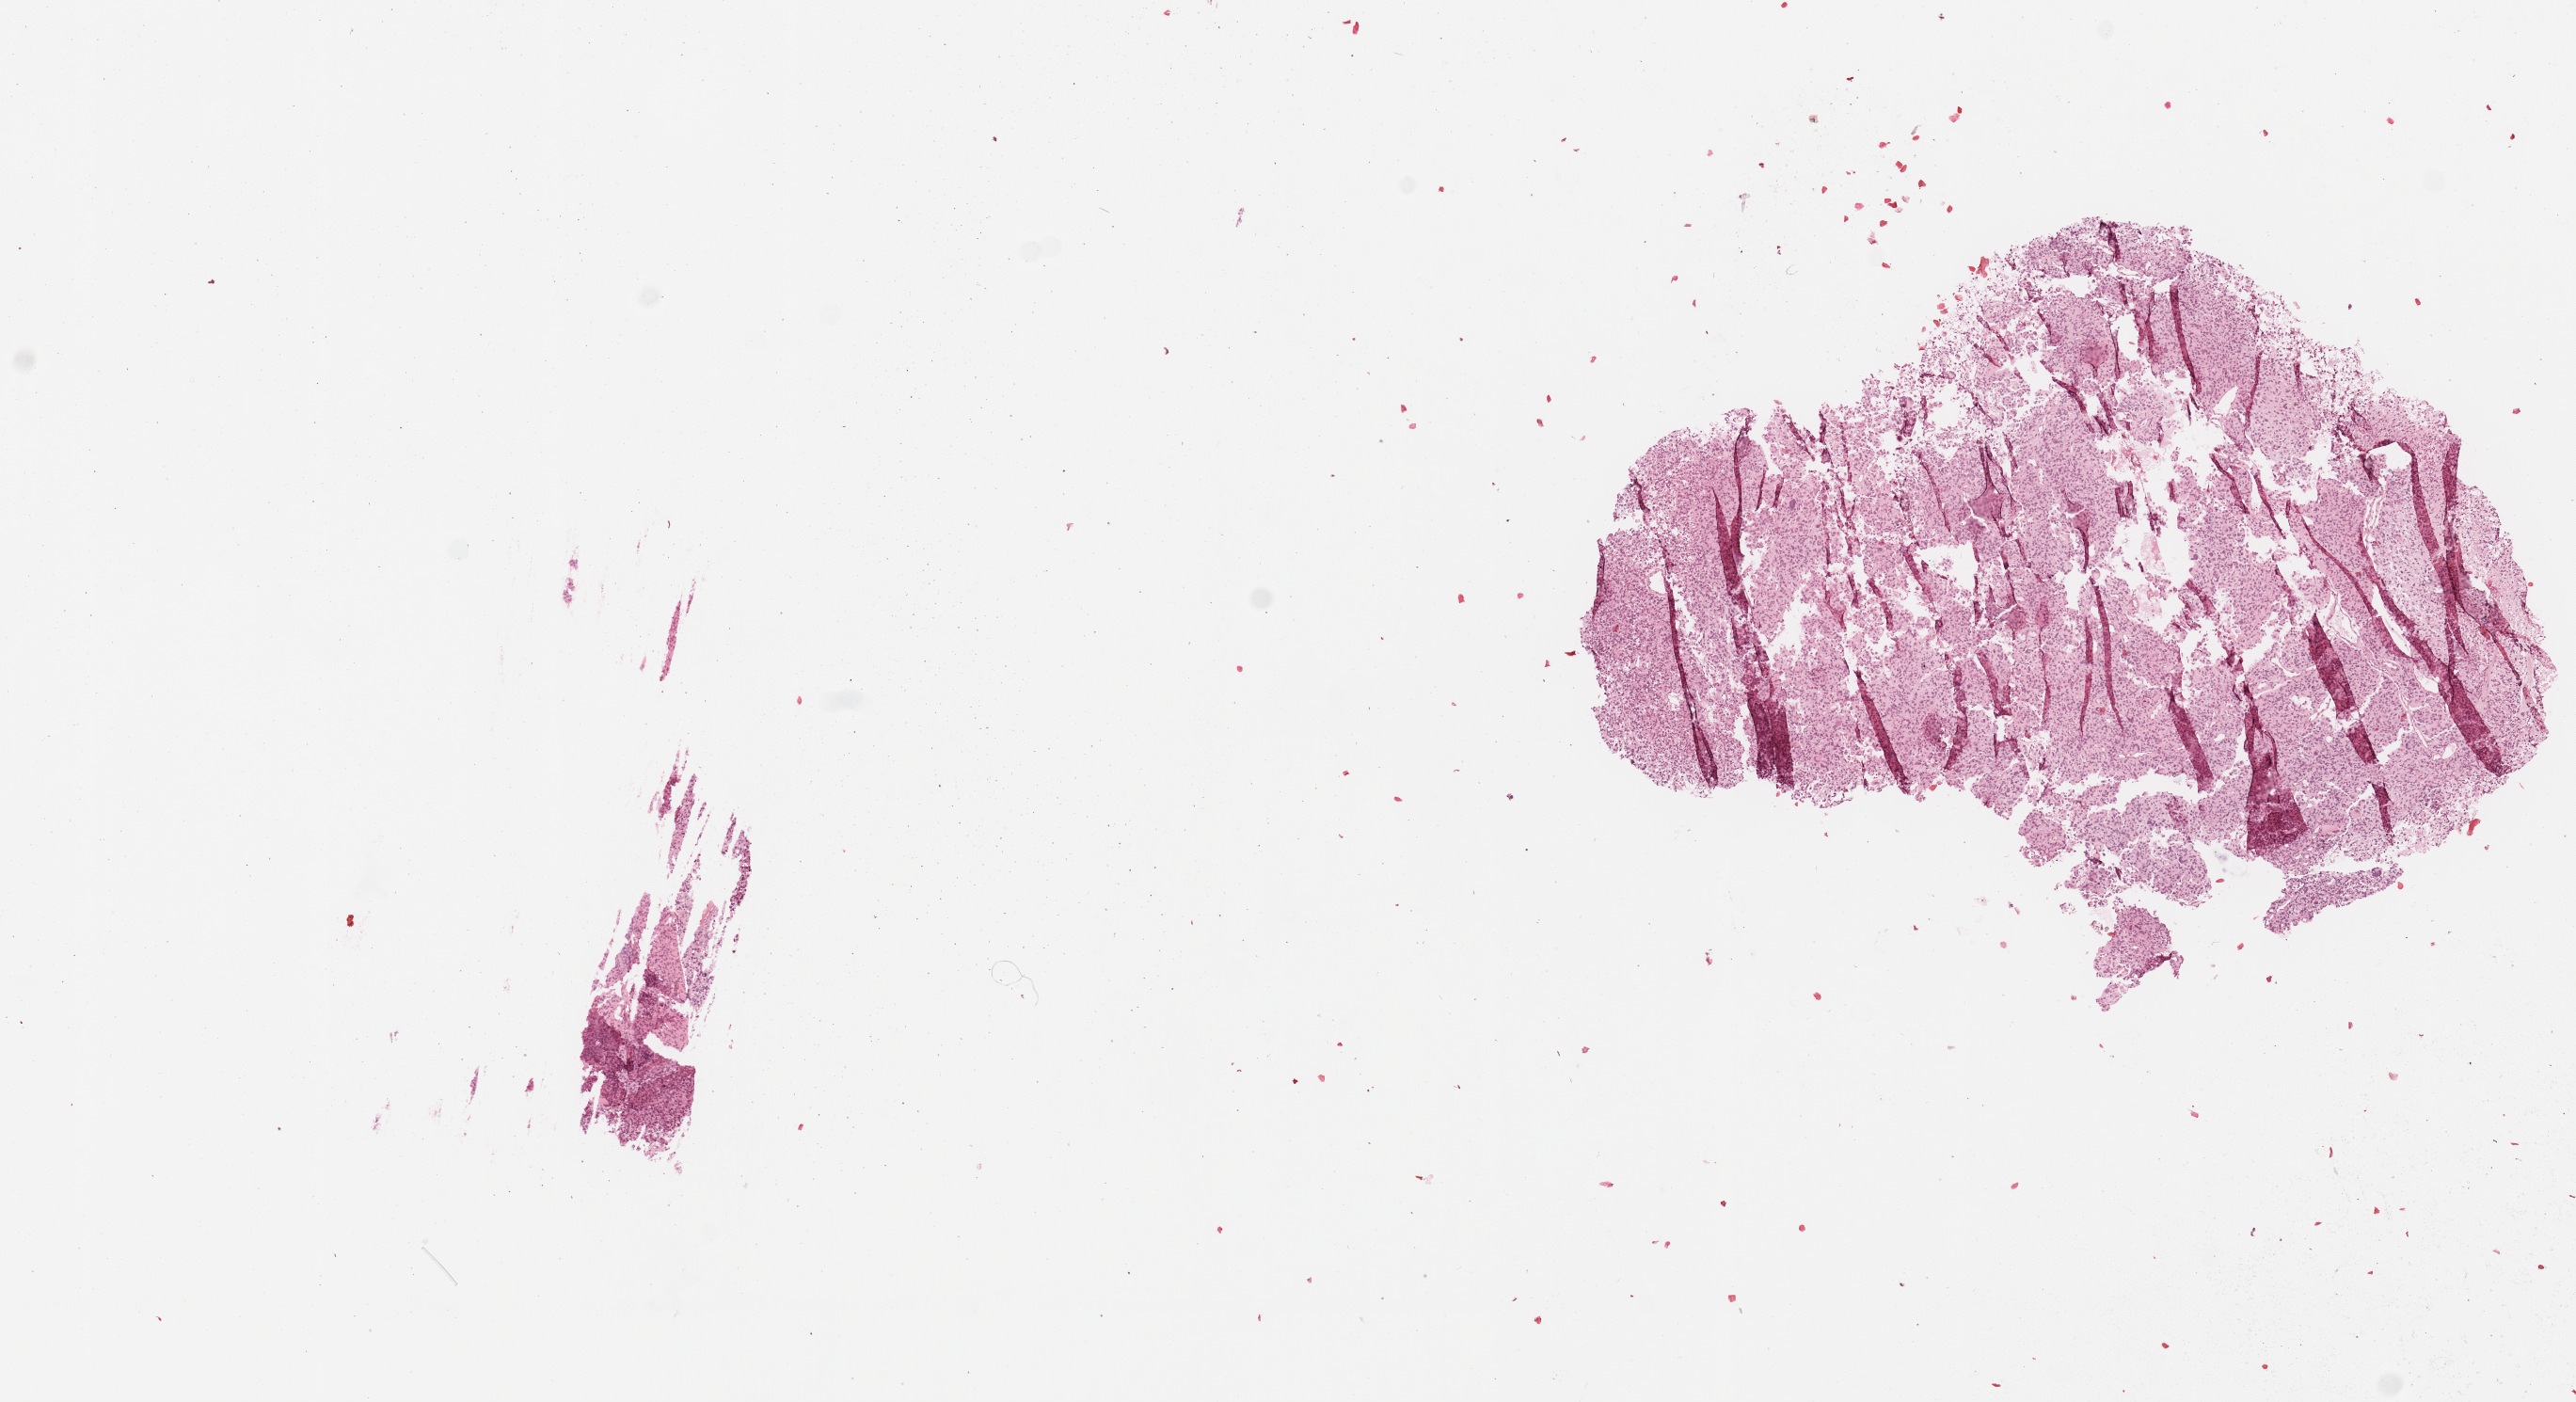
H&E-stained whole-slide image — a low-resolution overview of the entire scanned area, about 10.8 x 5.9 mm, tumour tissue sample, sampled site: brain. 67-year-old male patient. Pathologist review of this section (percent, as recorded): tumour nuclei 85%, necrosis 5%.
Diagnosis: Glioblastoma.